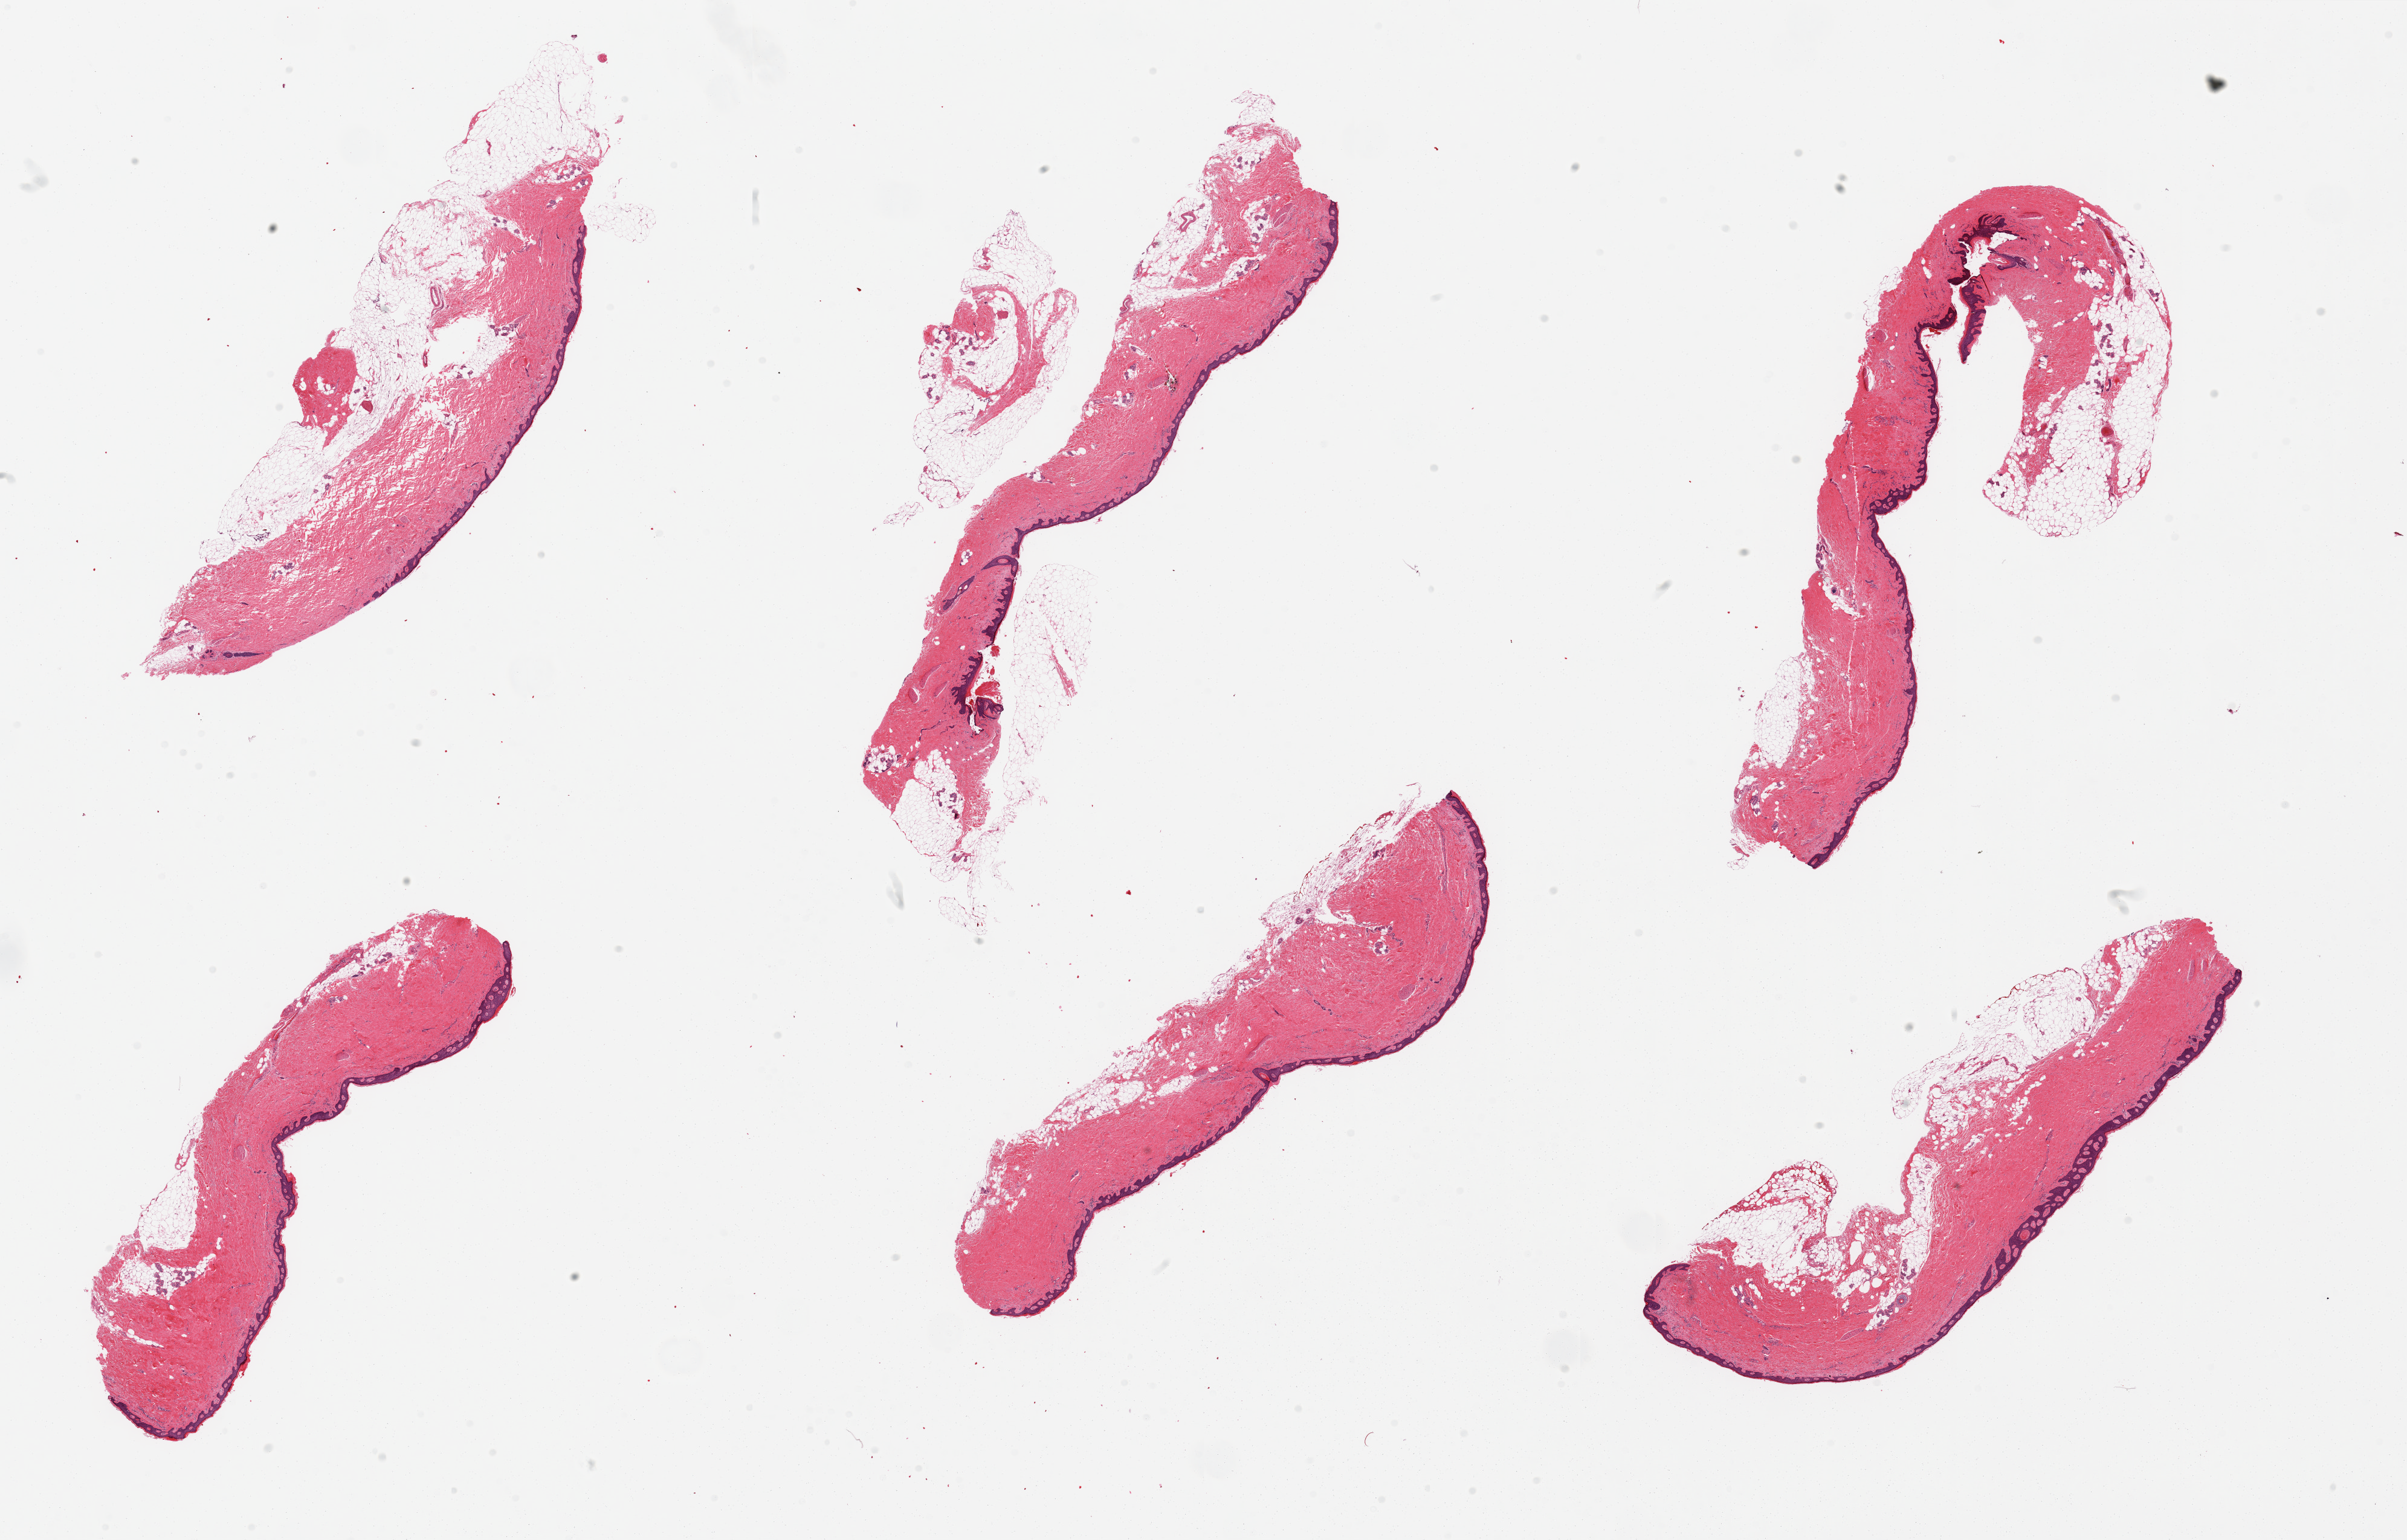
Hematoxylin and eosin (H&E) whole-slide image — whole scanned area (about 31.5 x 20.2 mm, acquisition: 20x scan) shown as a low-resolution overview; PAXgene-fixed, paraffin-embedded tissue; target tissue: skin of suprapubic region; donor tissue sample.
Review note (as recorded): 6 pieces, ~sqaumous epithelium is ~60 microns; adherent fat up to 1-1.5mm on sections.